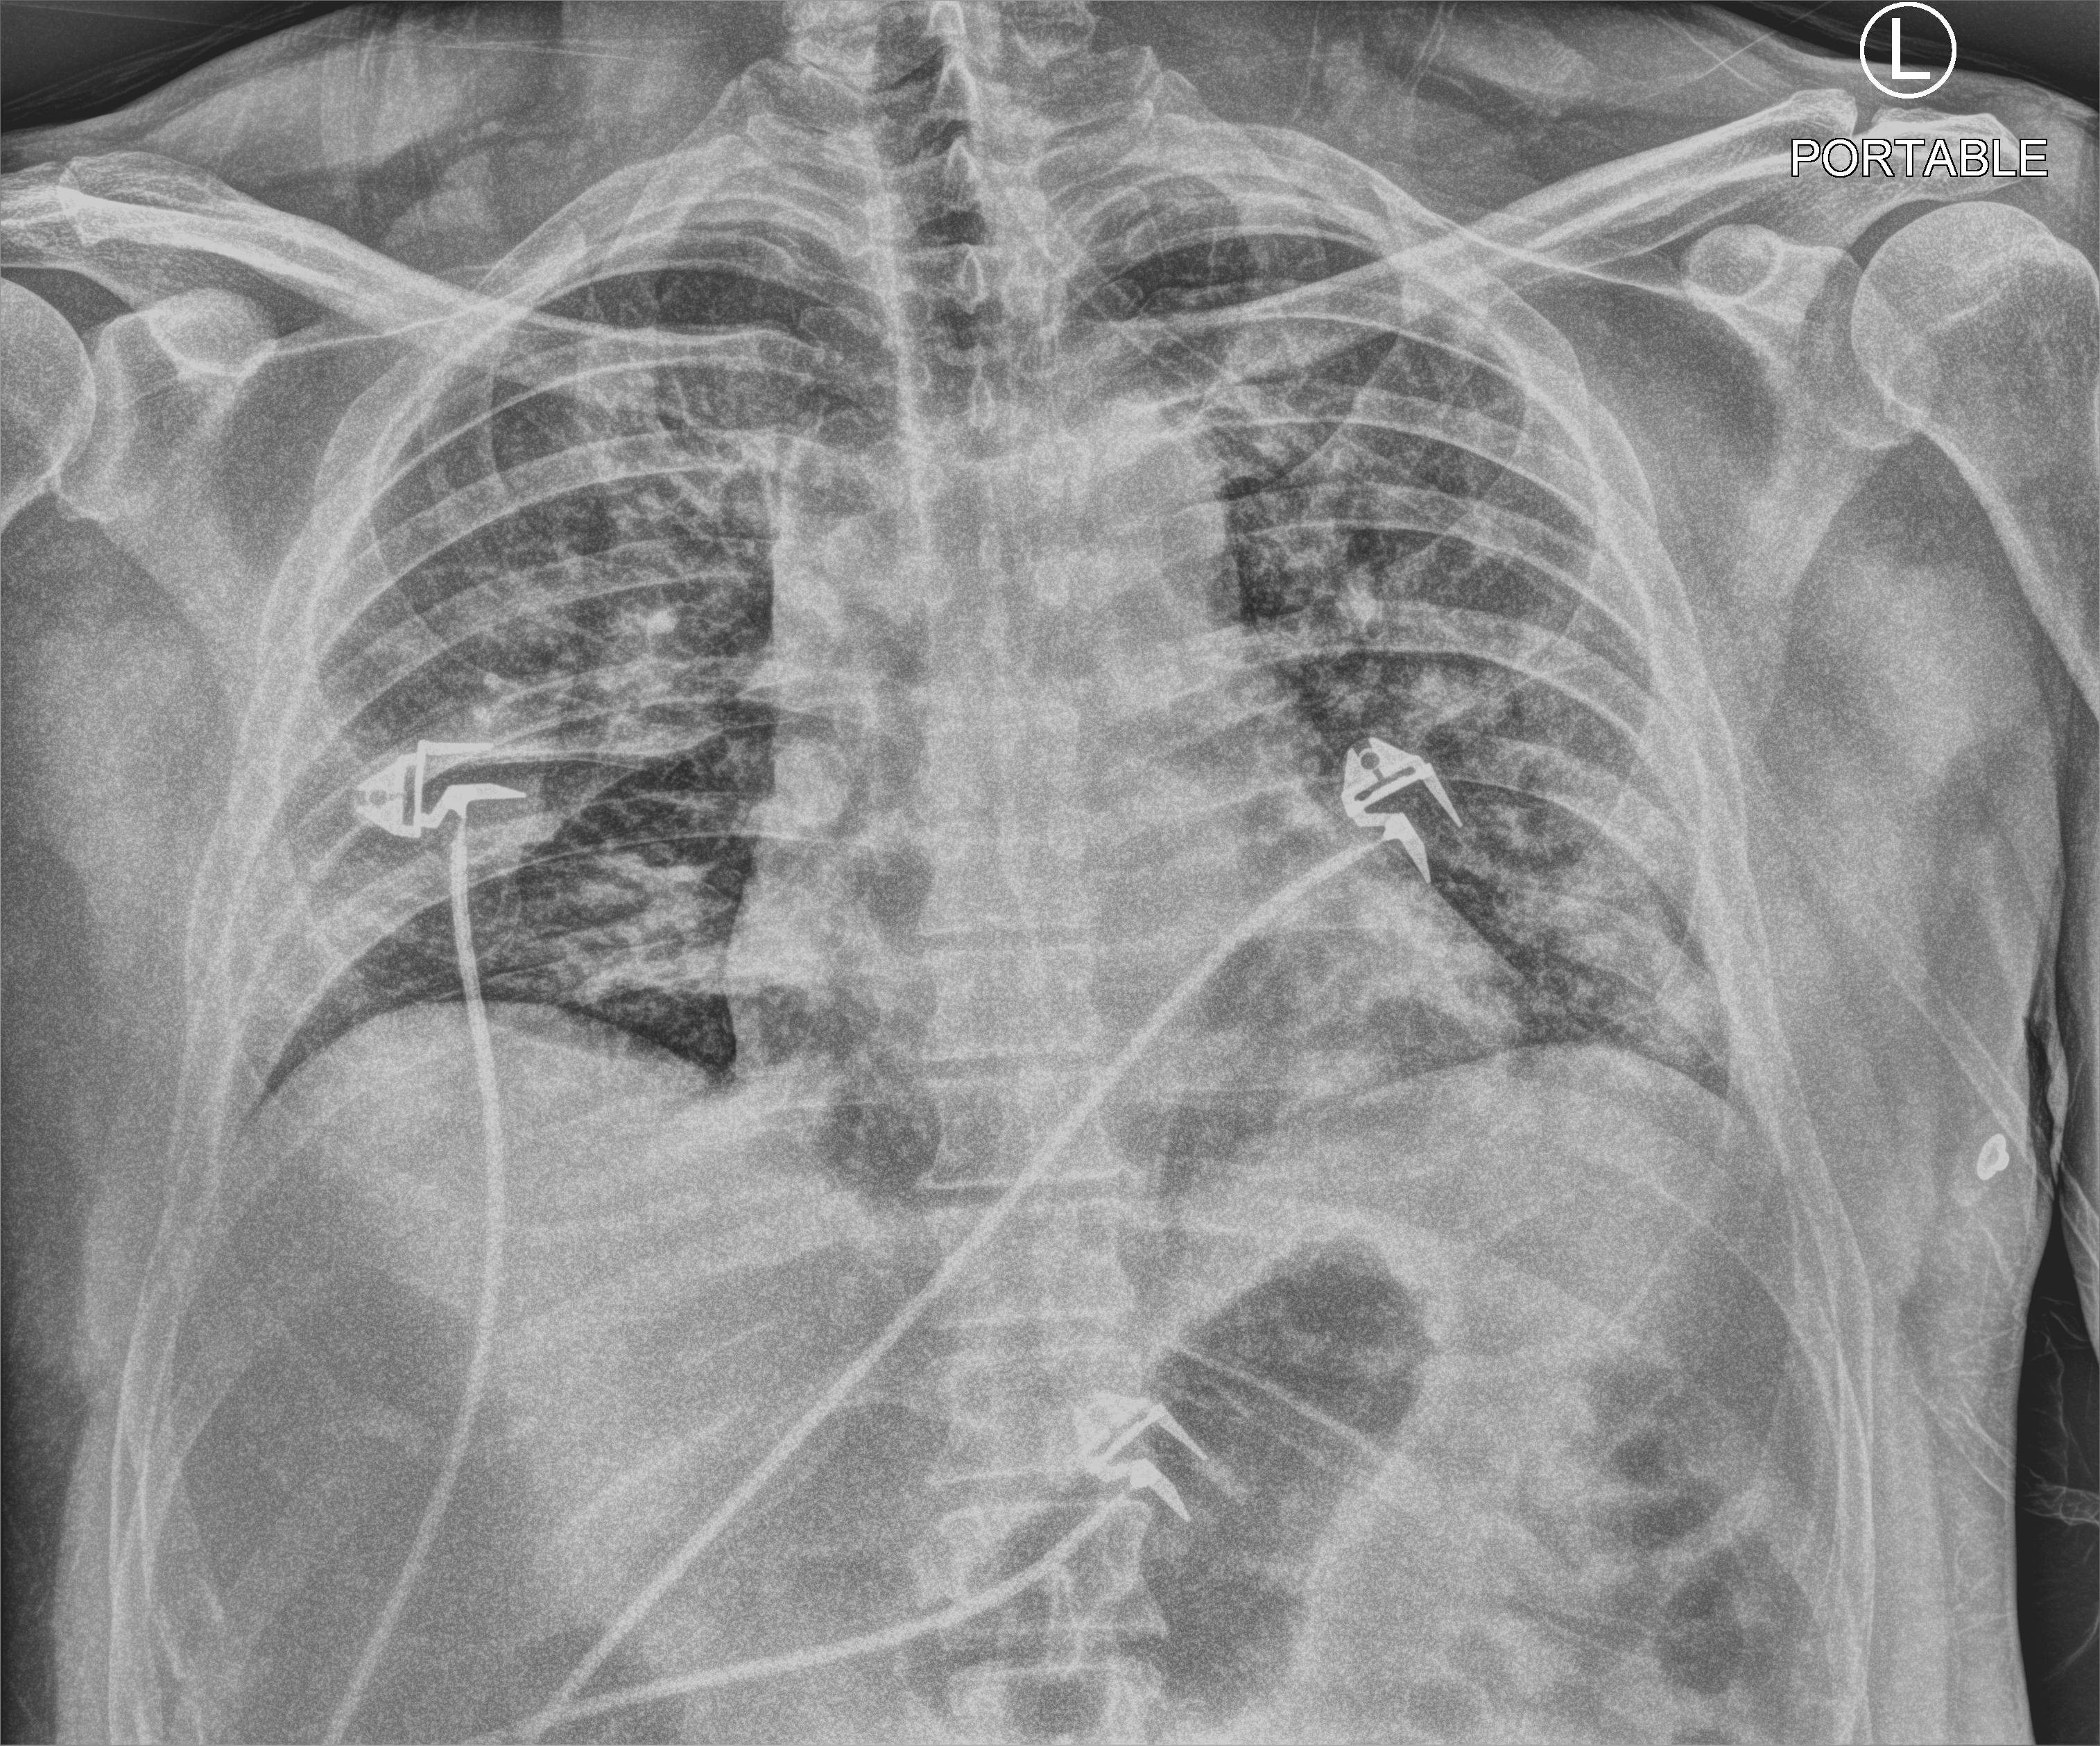
Portable chest radiograph. Male patient hospitalised with COVID-19, age 18–59 years.
Hospital-stay facts (about this admission, not read from this image; timing relative to this image not recorded):
- mechanically ventilated during this hospital stay: no